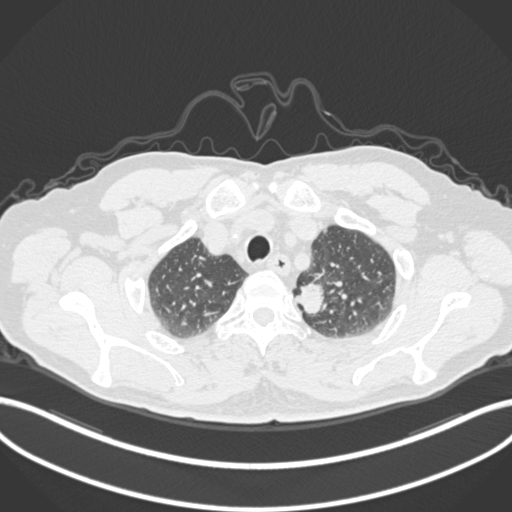
Chest CT, one axial slice; position 275 of 306 along the scan axis; 120 kVp; lung window (W 1500 / L -600 HU); 1 mm slice thickness; 512 × 512 image matrix, field of view 400 × 400 mm. Patient: male, 64 years. From the clinical record (not read from this slice): clinical TNM (as recorded): T1c N0 M0.
Structures marked on this image (rectangle marked by the reading radiologist):
- lung tumour (recorded histology: adenocarcinoma): bounding box [x1, y1, x2, y2] px = [292, 276, 330, 317]